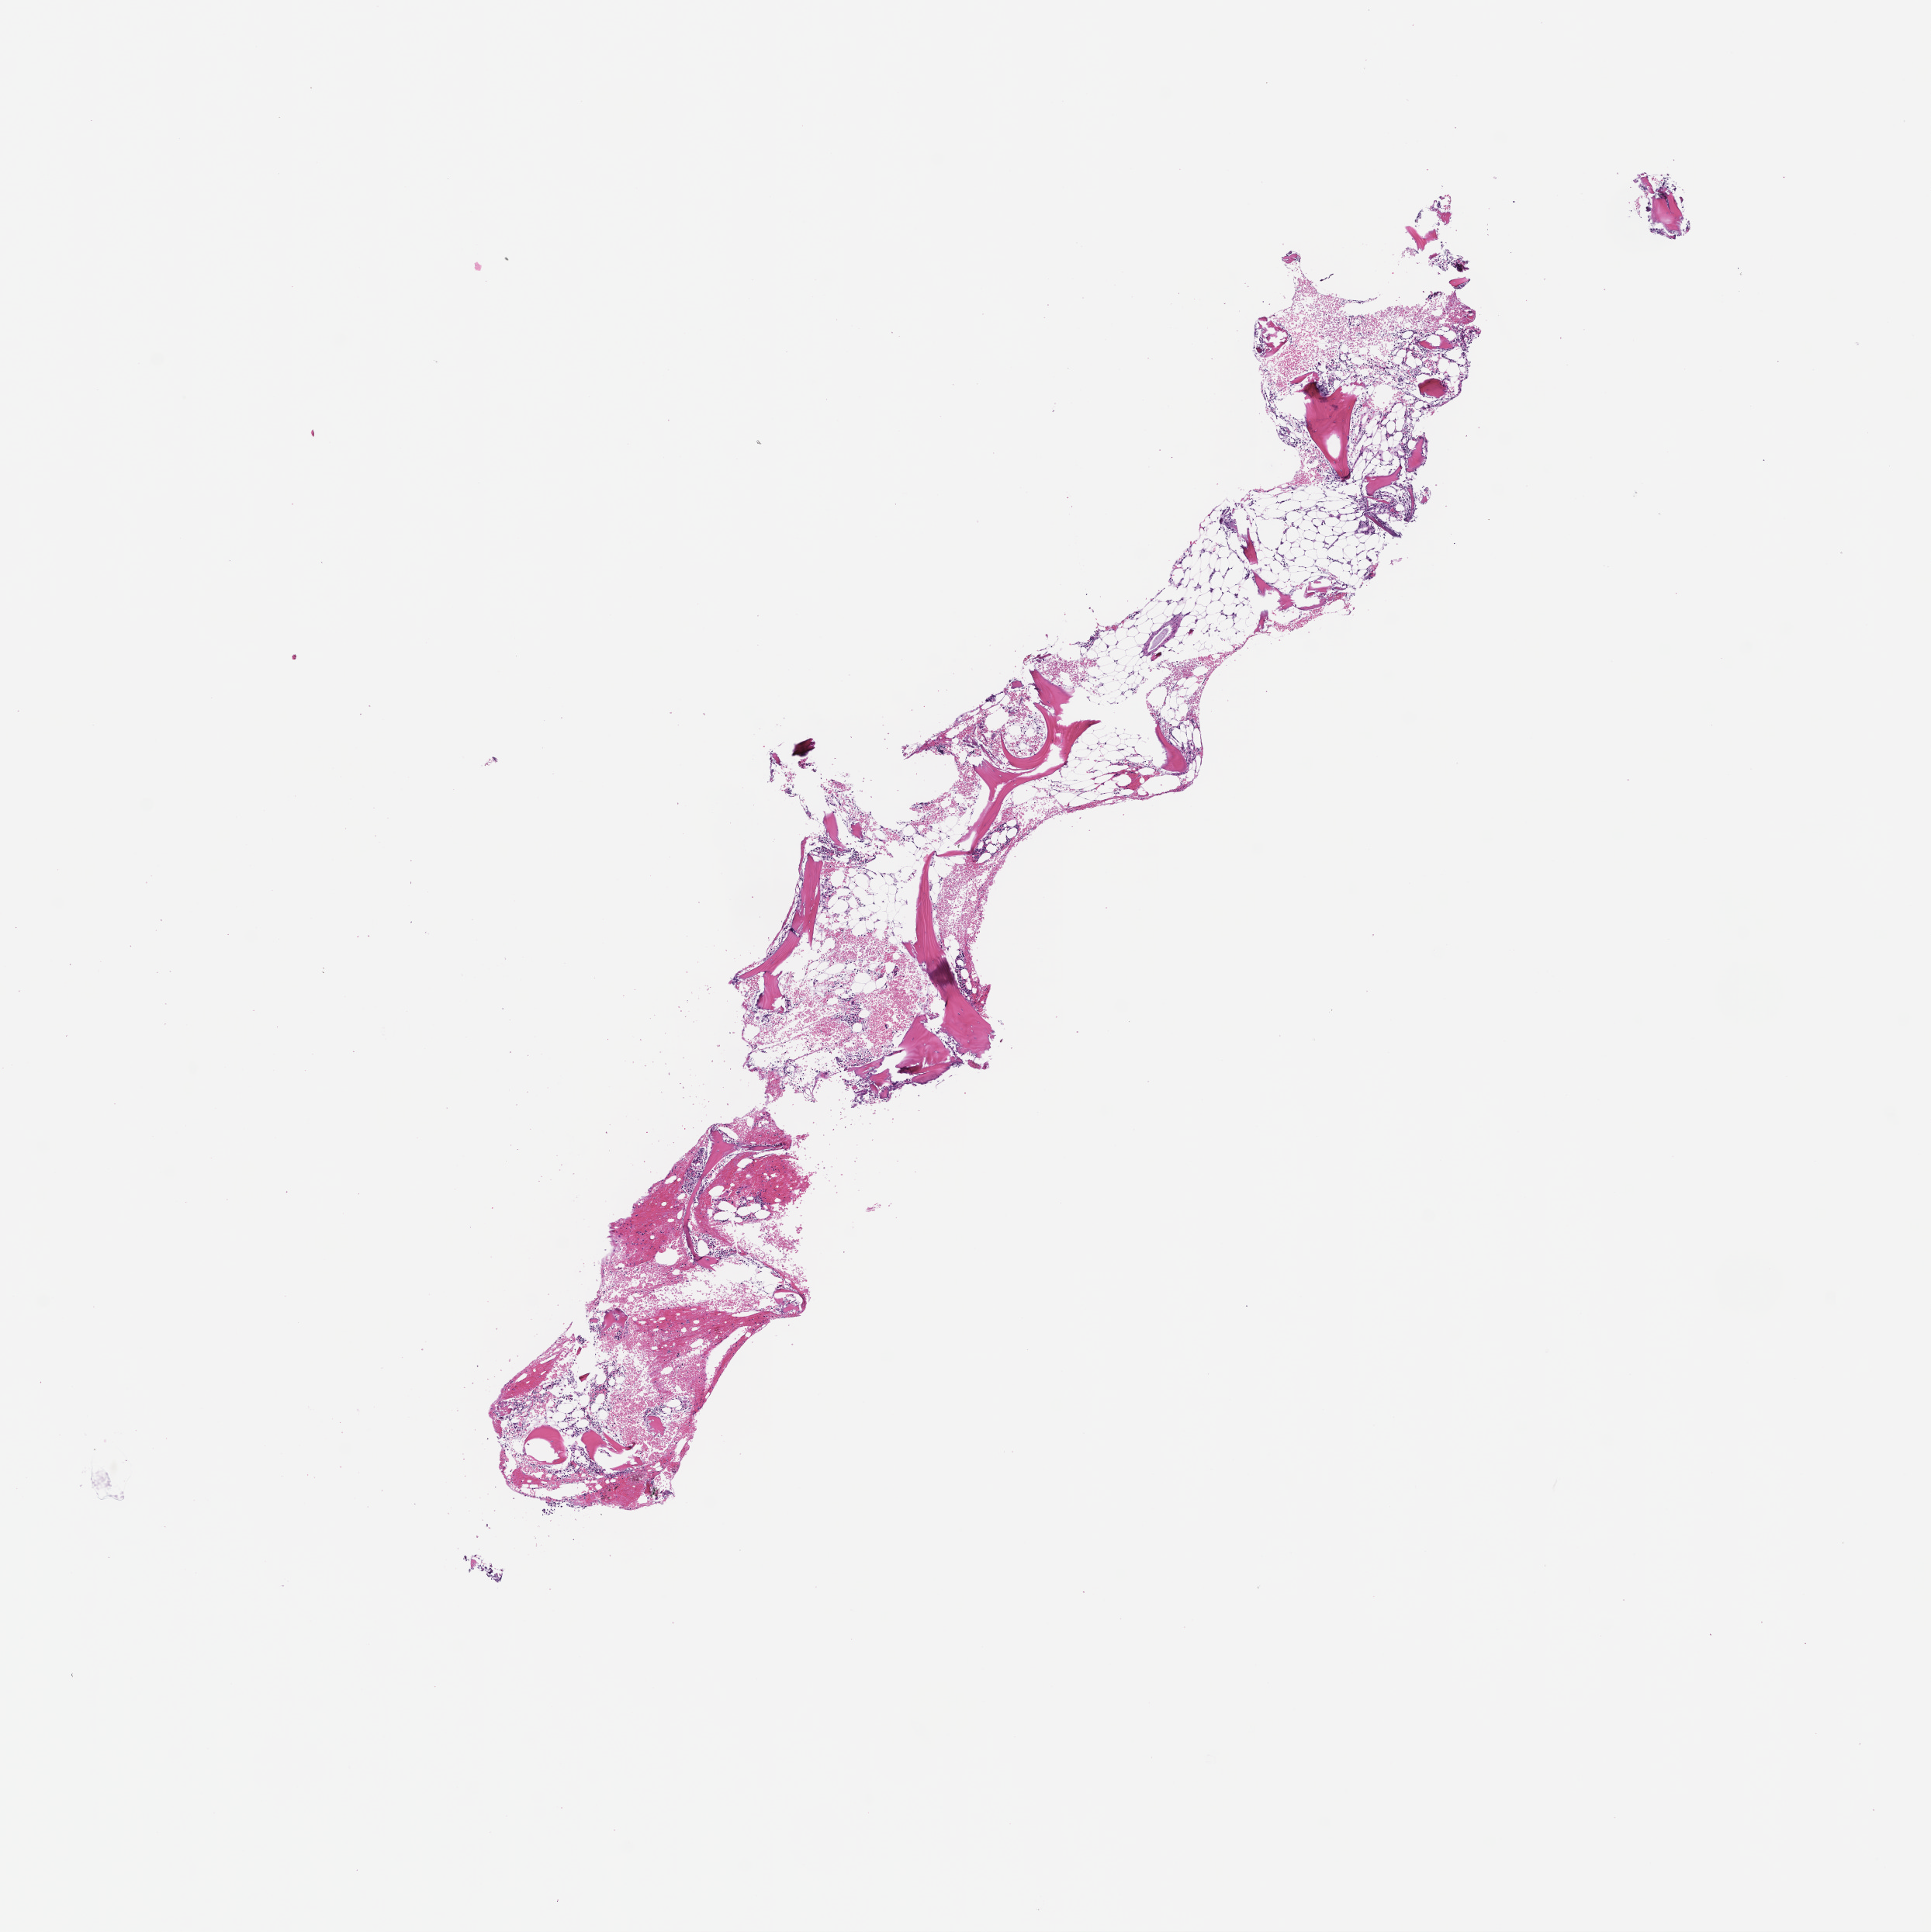
Hematoxylin and eosin (H&E) whole-slide image, a low-resolution overview of the entire scanned area, about 10.1 x 10.1 mm; formalin-fixed, paraffin-embedded (FFPE) tissue; site: bone marrow. Female patient.
• this section: primary tumour tissue
• diagnosis: Plasma Cell Myeloma